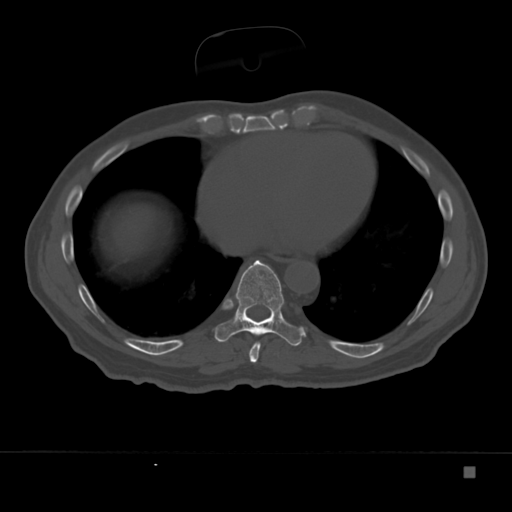
CT including the spine, one axial slice. Position 192 of 332 along the scan axis. Reconstruction kernel Br40s. Bone window (W 1800 / L 400 HU). 1.5 mm slice thickness. 512 × 512 image matrix. Patient: male, 72 years. Case-level facts recorded for this patient, not image findings: primary cancer: skeletal.
Annotated regions visible in this slice (semi-automatic segmentation, software-assisted and operator-edited):
- T8 vertebra: bounding box <248,342,261,363> (left, top, right, bottom; pixels)
- T9 vertebra: <215,260,305,346>